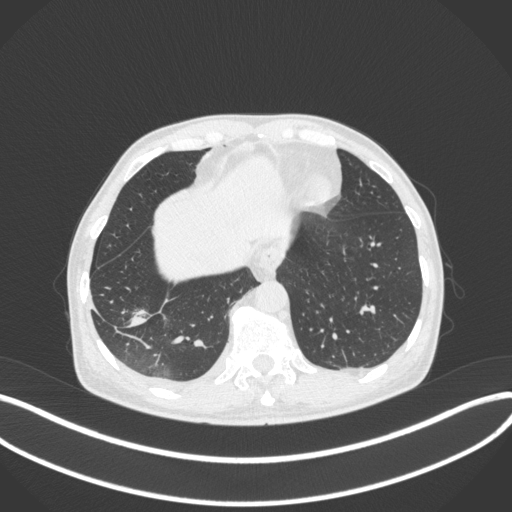
Chest CT, one axial slice; slice 81 of 385 in the series (ordered by position); reconstruction kernel B31f; 120 kVp; lung window (W 1500 / L -600 HU); 1 mm slice thickness; 512 × 512 image matrix, field of view 400 × 400 mm. Patient: male, 64 years. From the clinical record (not read from this slice): clinical TNM (as recorded): T3 N0 M0.
Annotated regions visible in this slice (bounding box drawn by a radiologist):
- lung tumour (recorded histology: adenocarcinoma): box from (x=124, y=300) to (x=156, y=332) px